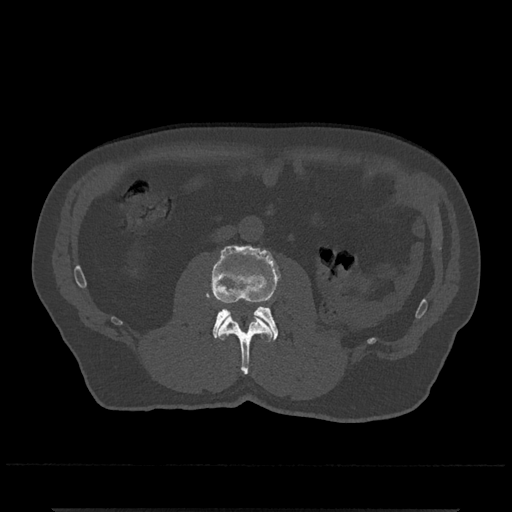
CT including the spine, one axial slice. Position 256 of 797 along the scan axis. 120 kVp. Bone window (W 1800 / L 400 HU). 0.5 mm slice thickness. 512 × 512 image matrix, field of view 393 × 393 mm. Male patient, age 67 years. Case-level facts recorded for this patient, not image findings: primary cancer: prostate.
Structures marked on this image (semi-automatic segmentation, software-assisted and operator-edited):
- L2 vertebra: box from (x=218, y=314) to (x=273, y=375) px
- L3 vertebra: (x=206, y=246)–(x=280, y=341)